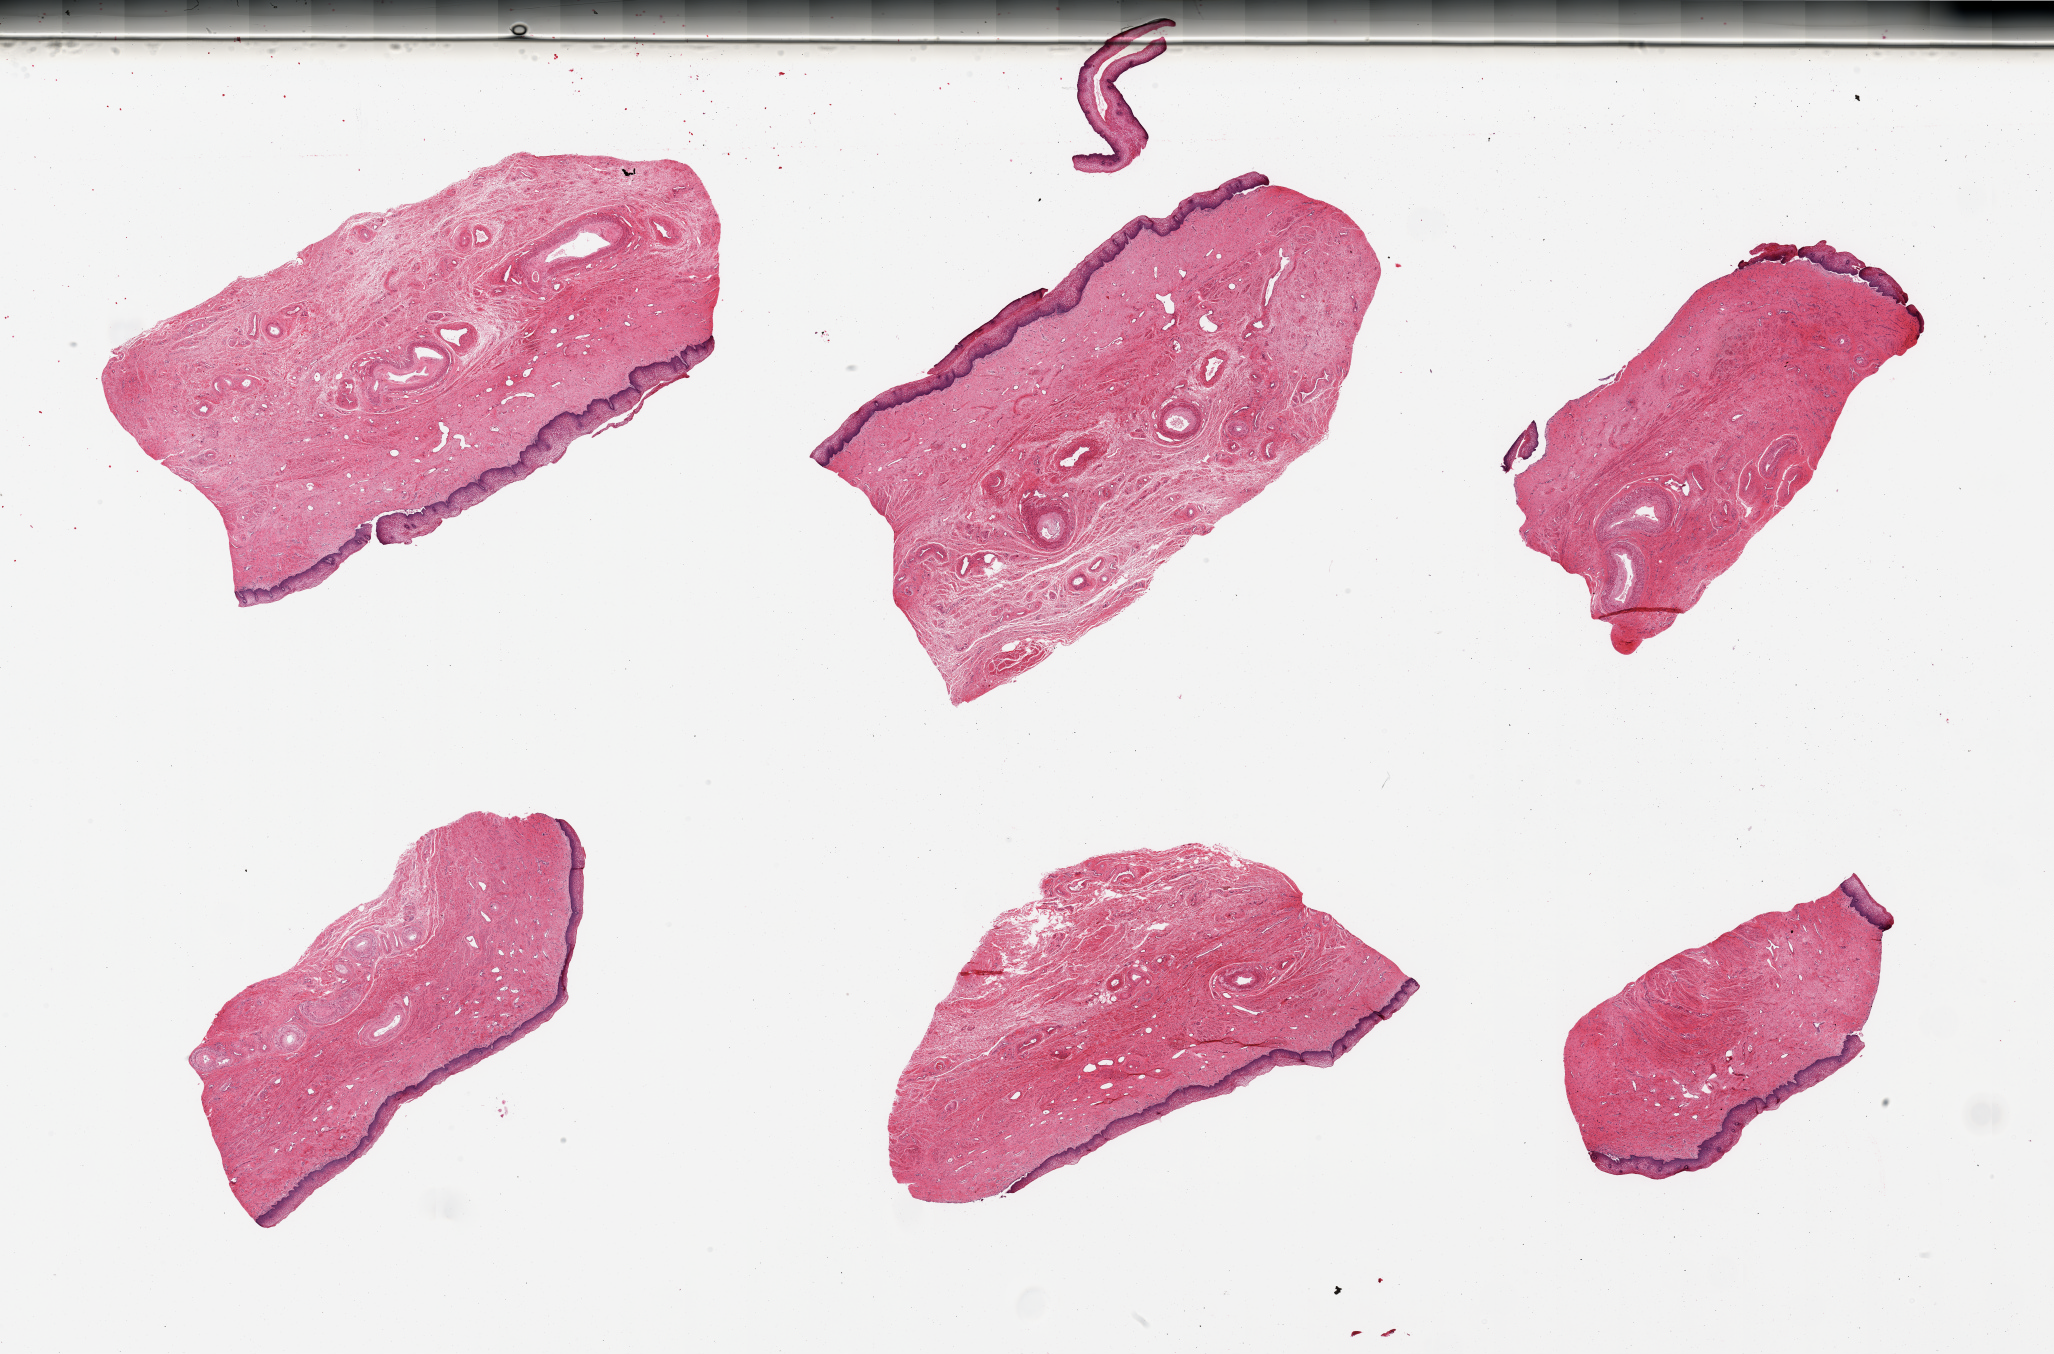
H&E whole-slide image, brightfield, low-resolution overview of the scanned area, about 32.5 x 21.4 mm. PAXgene-fixed, paraffin-embedded tissue. Sampled site (target tissue): vagina. Donor tissue sample.
Pathologist's review note for this sample: 6 pieces, squmous mucosa is ~0.2-0.3mm.